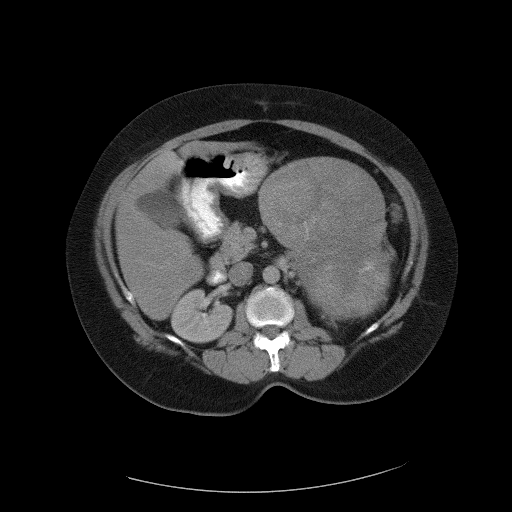
Contrast-enhanced abdominal CT, one axial slice. 120 kVp. Intravenous contrast given. Soft-tissue window (W 400 / L 40 HU). 5 mm slice thickness. 512 × 512 image matrix. Patient: female, 55 years. Case-level facts recorded for this patient, not image findings: diagnosis: adrenocortical carcinoma; tumour side: left adrenal.
Annotated regions visible in this slice (semi-automatically segmented with operator editing):
- mass: box from (x=260, y=158) to (x=388, y=320) px